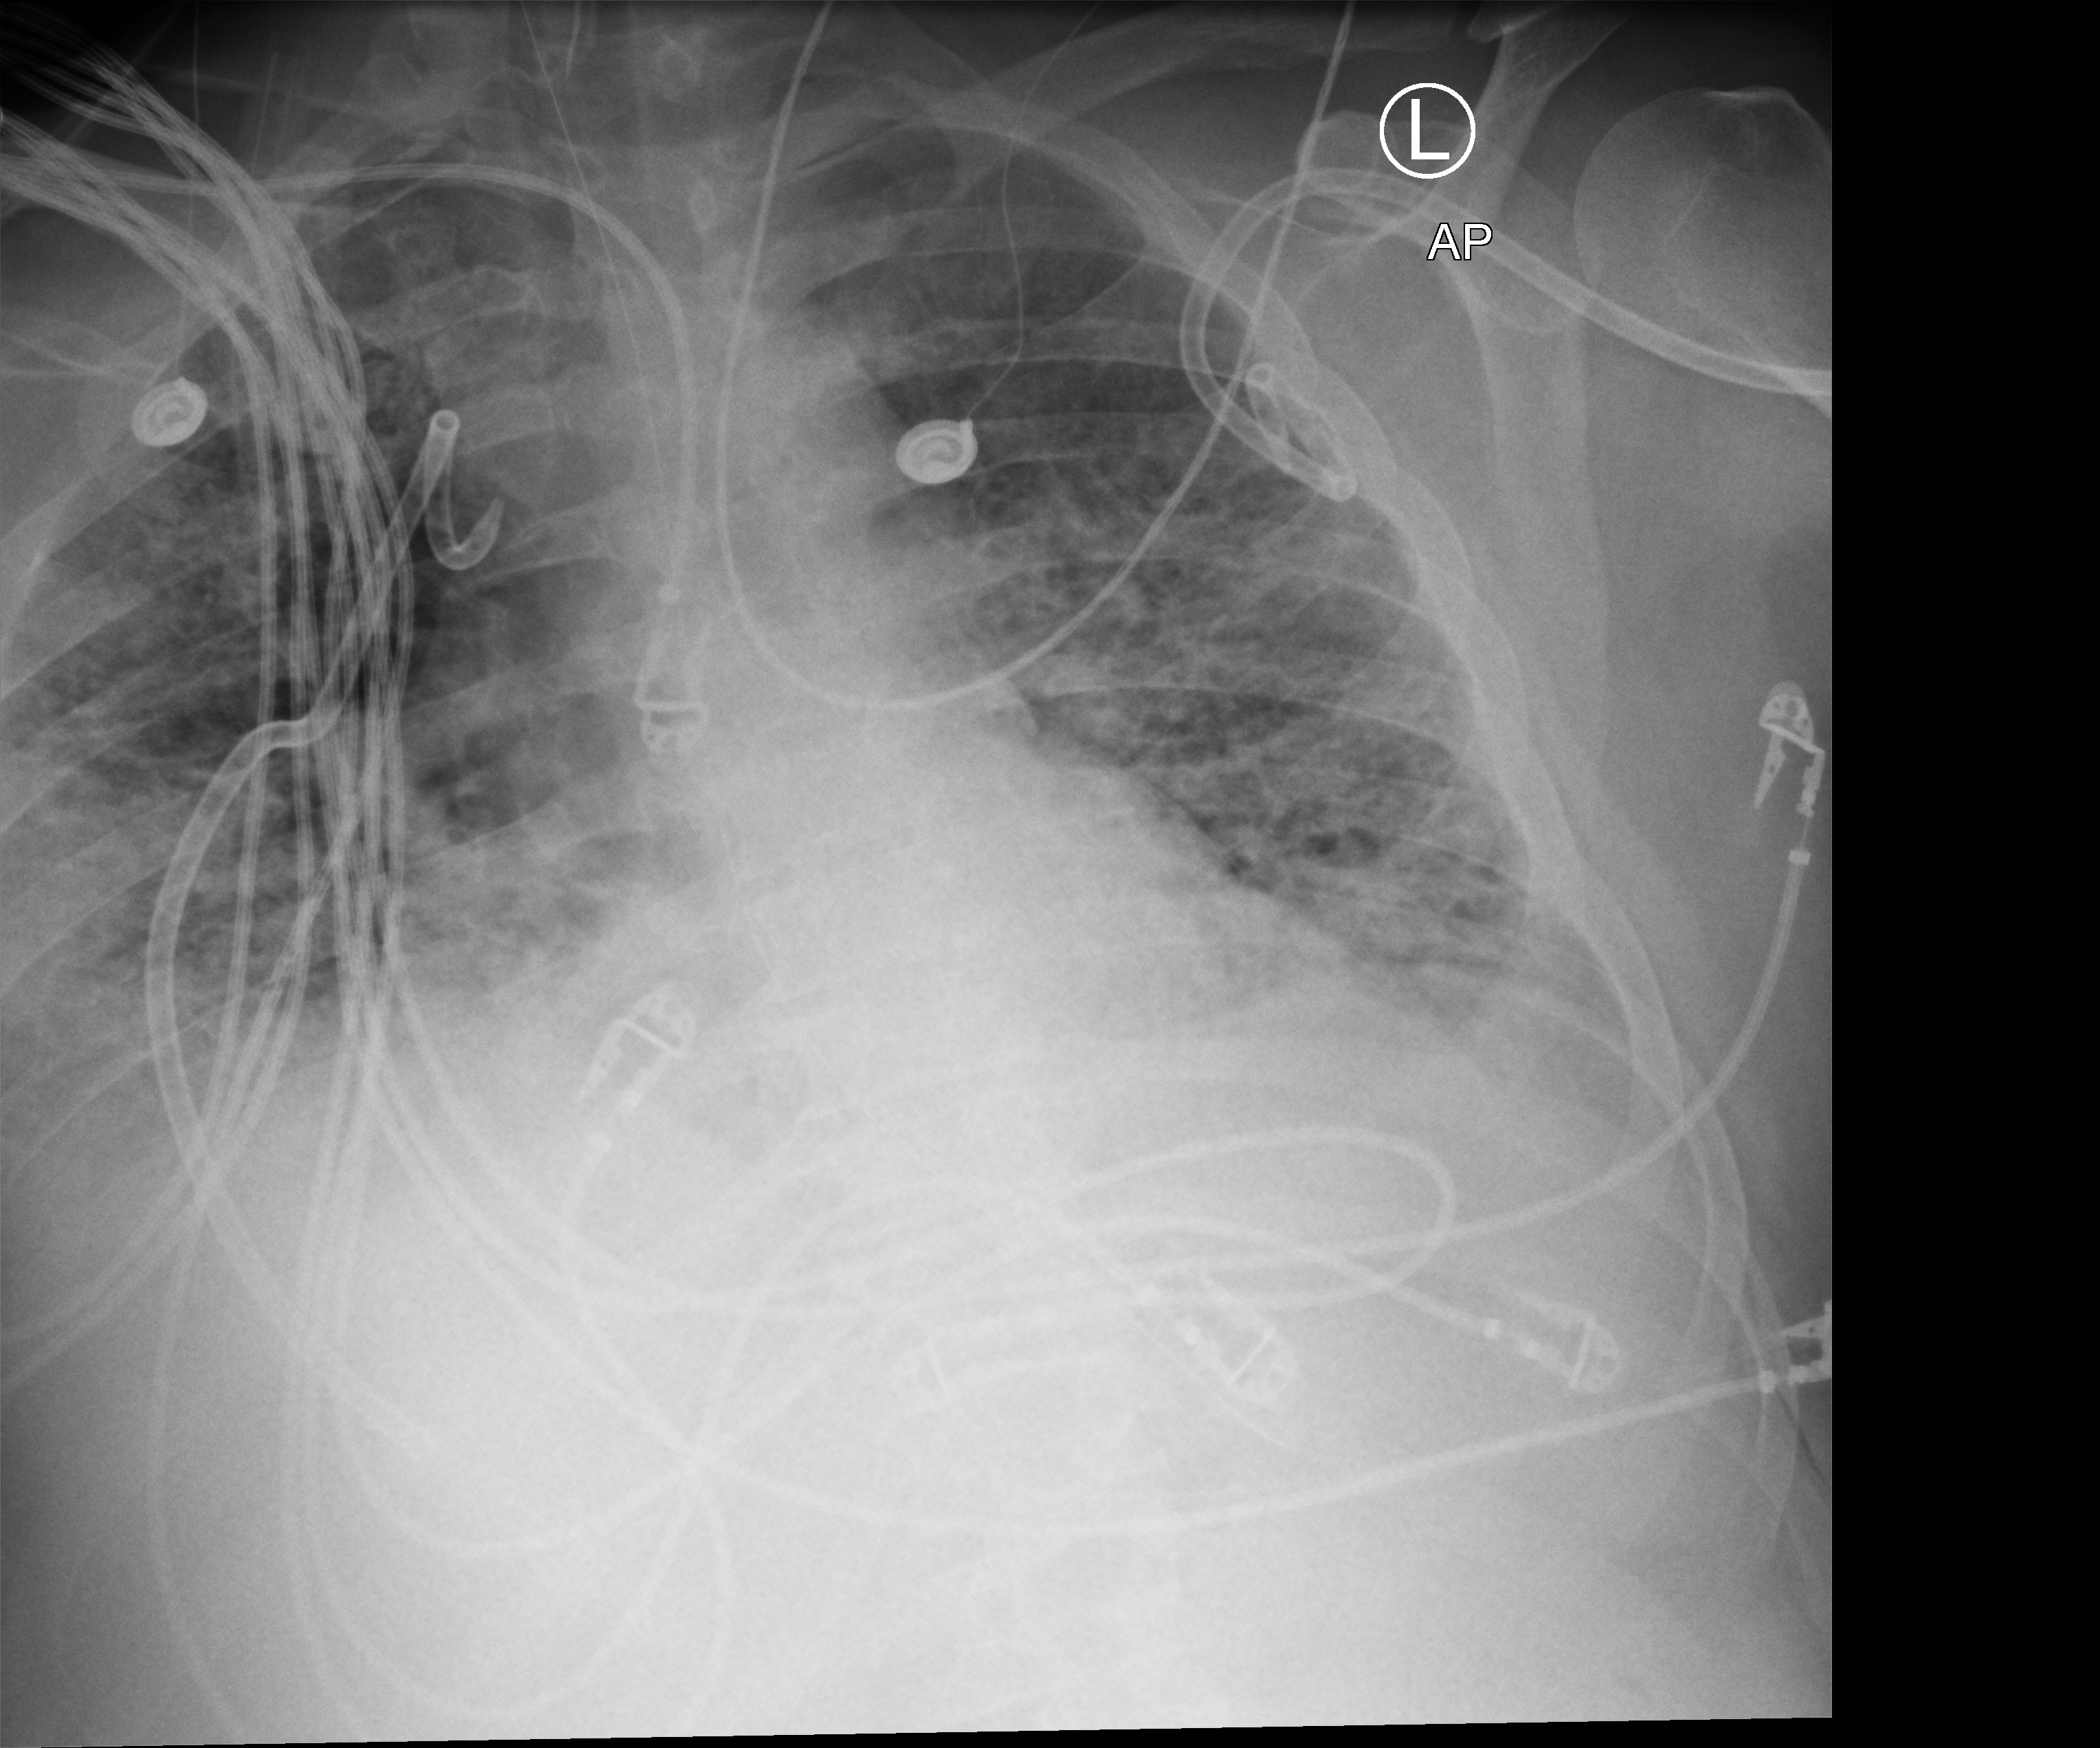
Bedside chest radiograph (computed radiography); anteroposterior (AP) projection. Adult patient hospitalised with COVID-19, age 18–59 years.
Hospital-stay facts (about this admission, not read from this image; timing relative to this image not recorded):
- mechanically ventilated during this hospital stay: yes